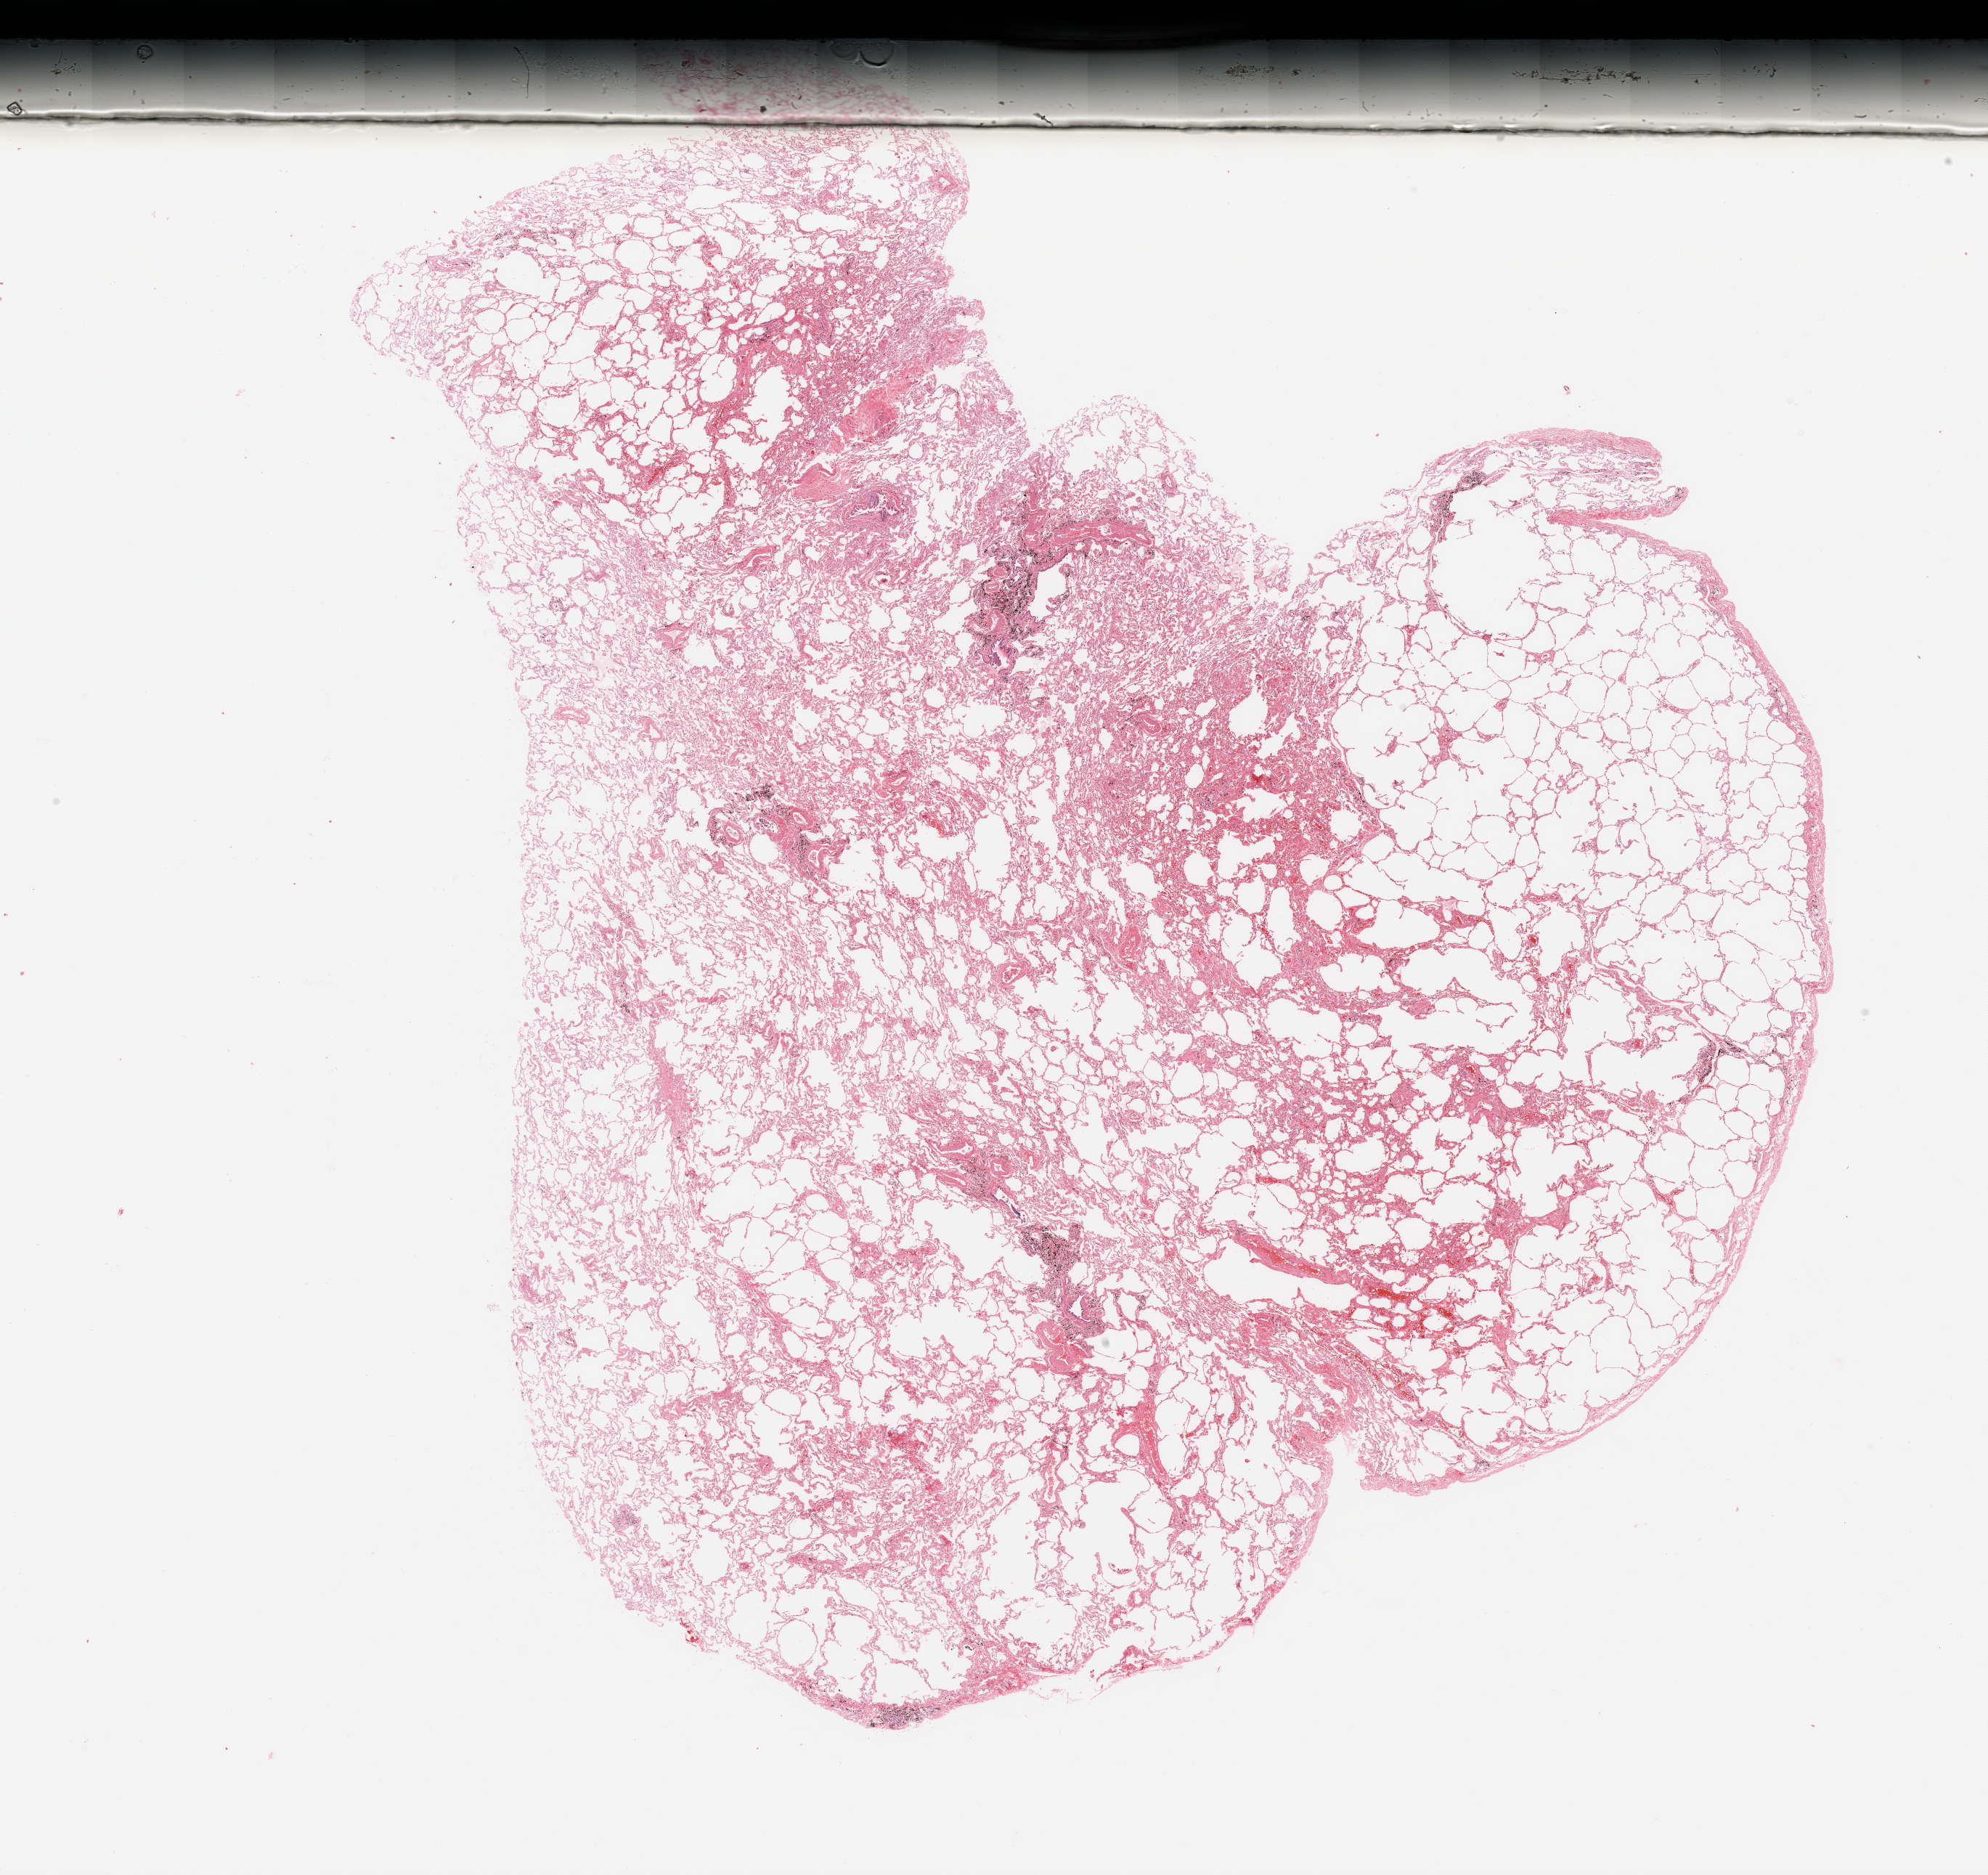
Digitized H&E tissue section (whole slide), low-resolution overview of the scanned area, about 21.7 x 20.4 mm (from a 20x scan). Lung, normal (non-tumour) tissue. Female, 55 y/o.
* this section: normal (non-tumour) tissue from the same patient
* patient diagnosis: Adenocarcinoma, NOS